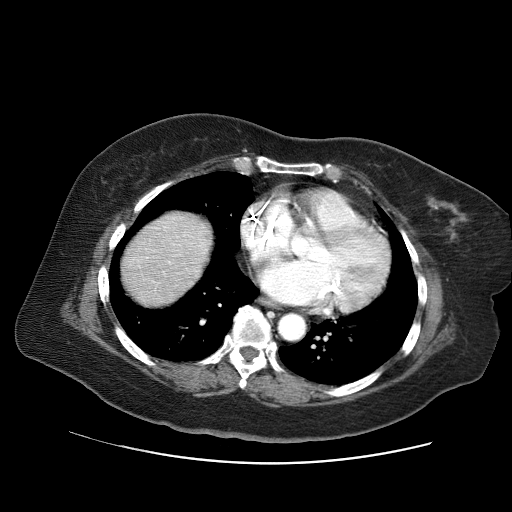
Contrast-enhanced abdominal CT (liver protocol), one axial slice; slice 64 of 71 in the series (ordered by position); soft-tissue window (W 400 / L 40 HU); 2.5 mm slice thickness; 512 × 512 image matrix. Case-level facts recorded for this patient, not image findings: diagnosis: hepatocellular carcinoma (patient treated with transarterial chemoembolisation; whether this scan precedes or follows treatment is not stated here); TNM stage (as recorded): Stage-II; Child-Pugh class: A; tumour differentiation: poorly differentiated; tumour nodularity: multinodular.
Annotated regions visible in this slice (semi-automatic segmentation, software-assisted and operator-edited):
- abdominal aorta: bounding box [x1, y1, x2, y2] px = [278, 314, 303, 339]
- liver parenchyma outside the tumour (the mass and vessels are separate outlines, so this box may not span the whole liver): [122, 210, 210, 304]